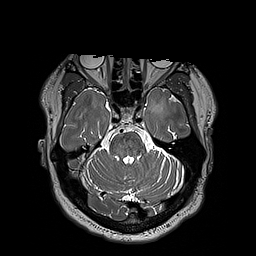
Brain MRI from a brain-tumour surgery series, one axial slice; position 132 of 192 along the scan axis; 1 mm slice thickness; 256 × 256 image matrix. From the clinical record (not read from this slice): histopathology: Astrocytoma; WHO grade: 3; IDH mutation: yes.
Outlined on this slice (outlined manually by an expert reader):
- tumour: bounding box (x1, y1, x2, y2) in pixels: (150, 98, 165, 115)